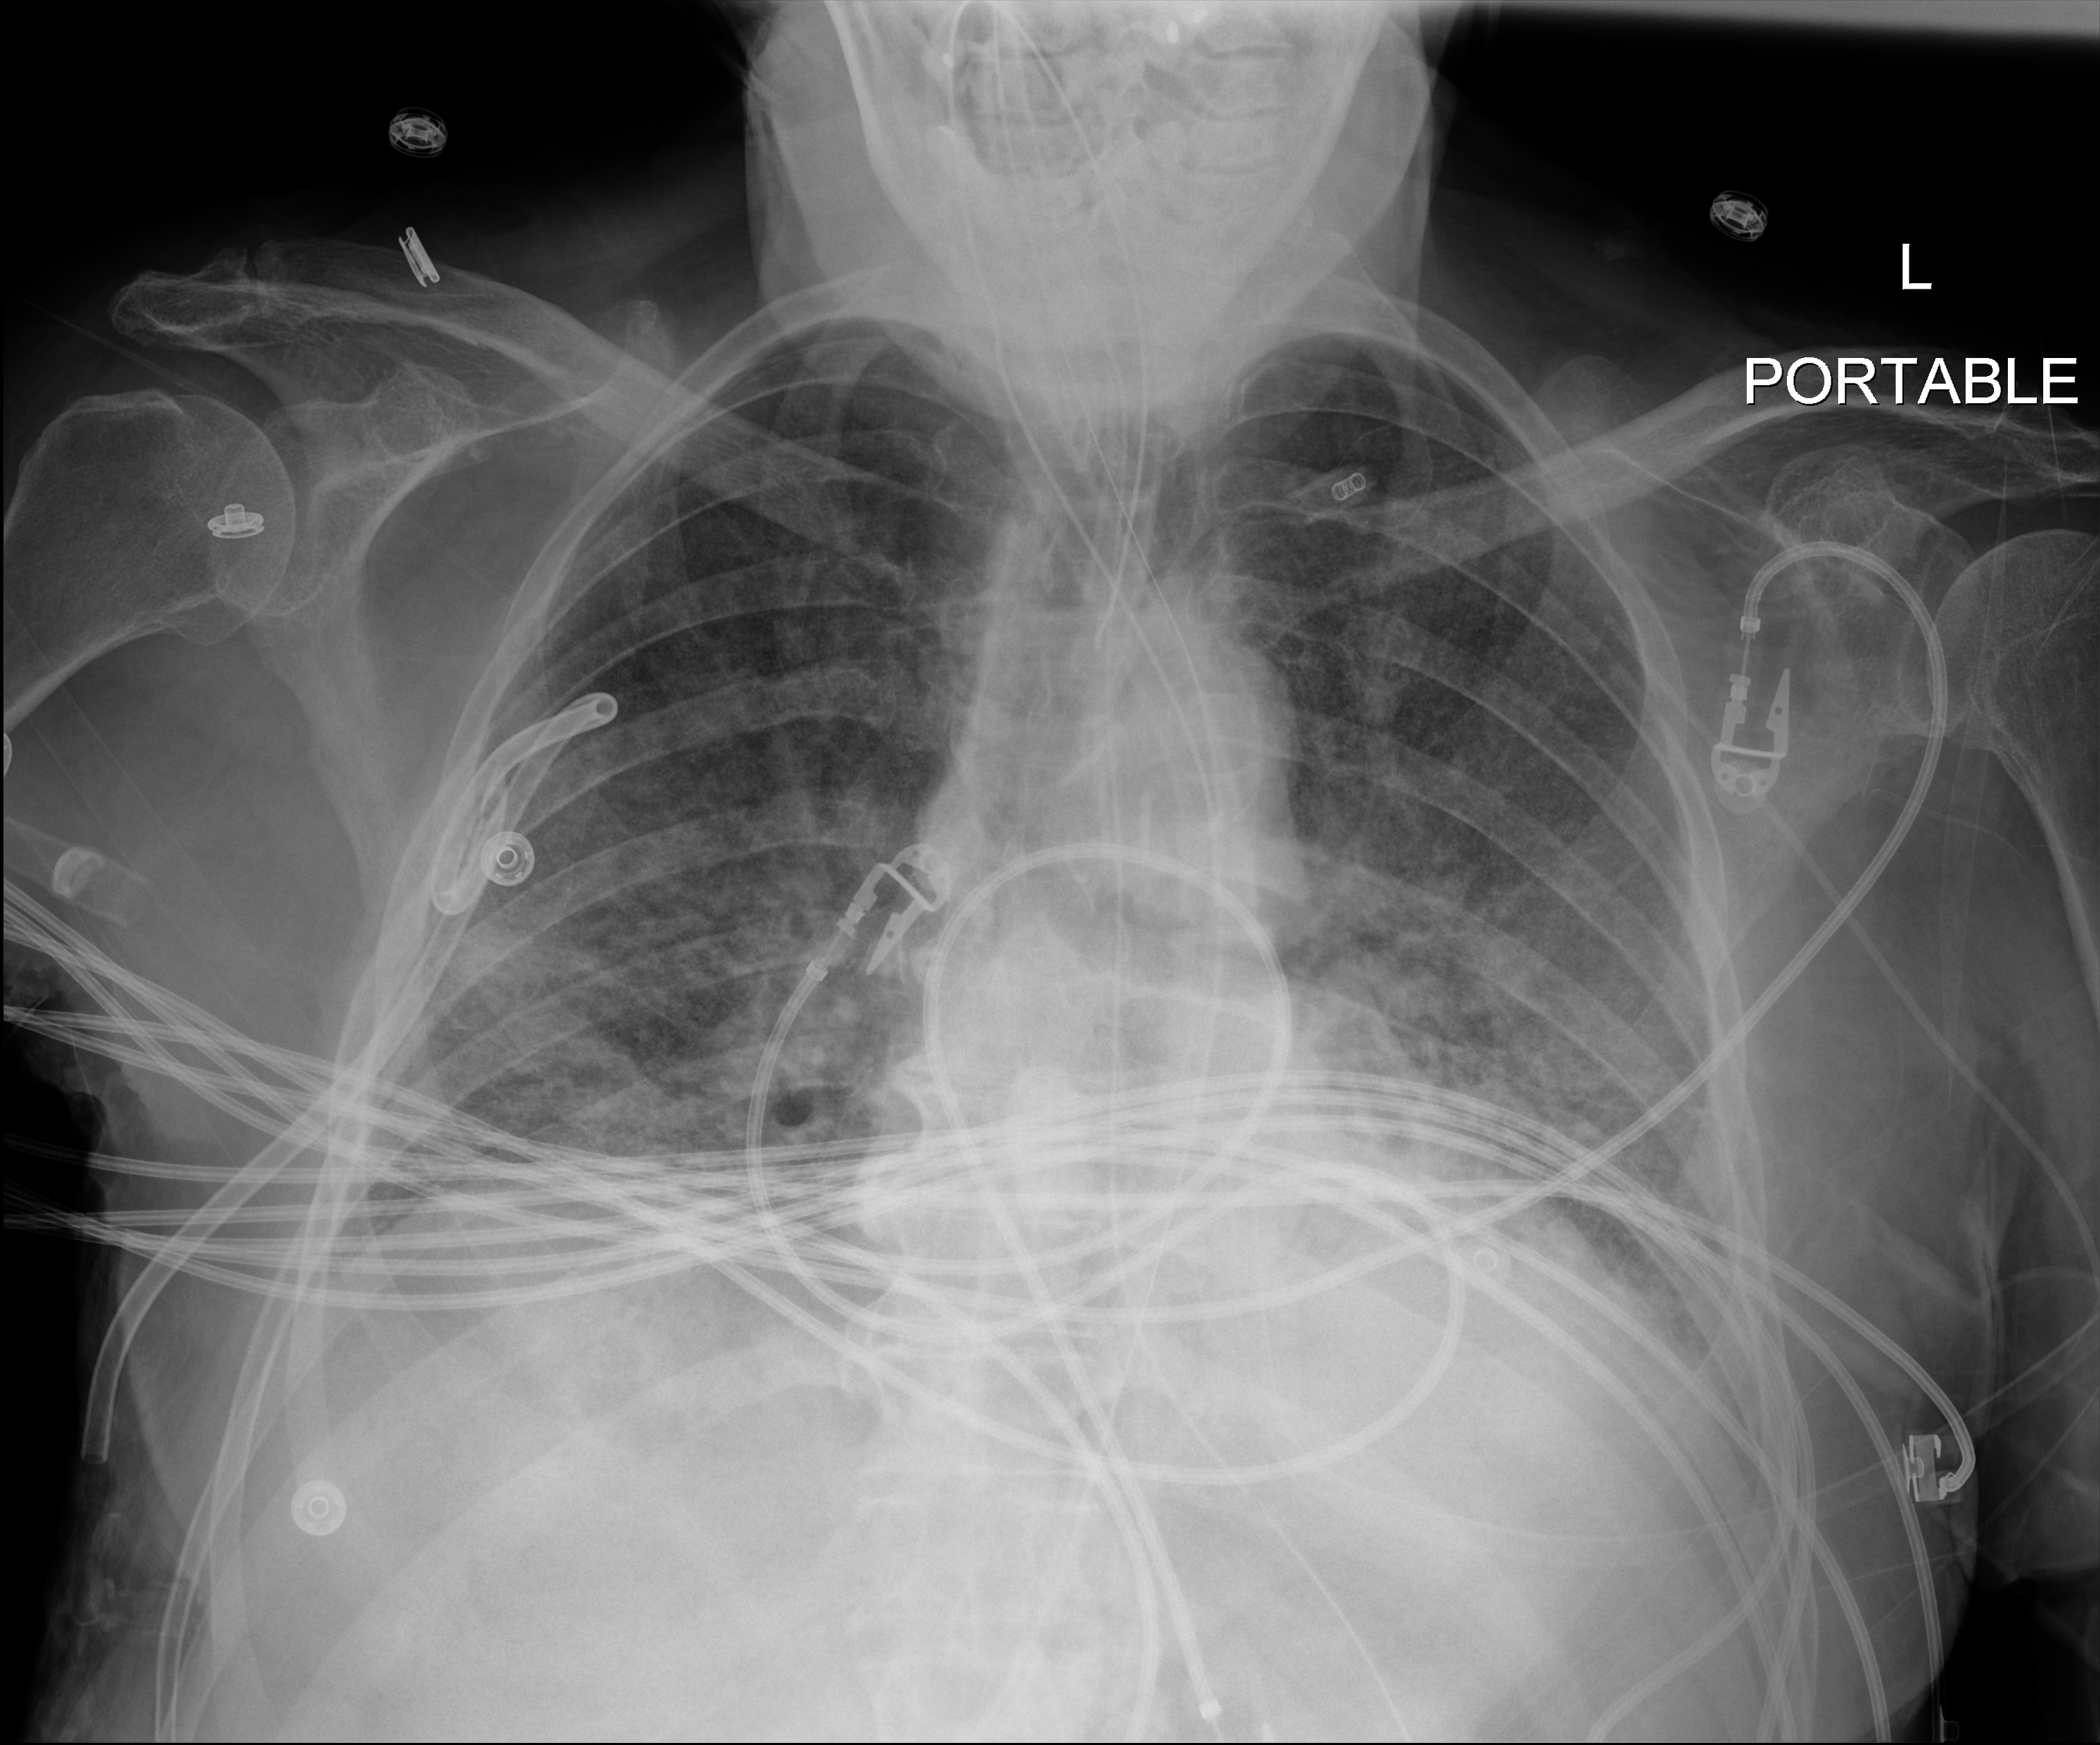
Portable chest radiograph. Male patient hospitalised with COVID-19, age 75–90 years.
Admission-level facts for this patient (not findings on this image; timing relative to this image not recorded):
- COPD (admission record): no
- hypertension (admission record): yes
- length of hospital stay: 23 days